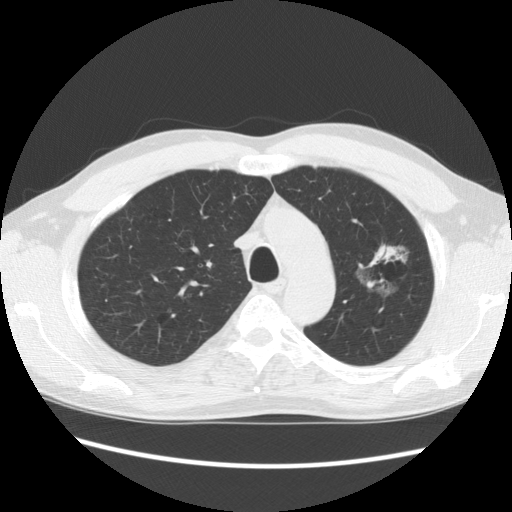
Low-dose screening chest CT, axial slice; second annual screen; lung window (W 1500 / L -600 HU); 2.5 mm slice thickness; 140 kVp; slice 104 of 139 in the series; 512 × 512 image matrix. Male, age 61 years at enrolment. Former smoker at enrolment.
Lesion marked by an expert reader, bounding box [x1, y1, x2, y2] px = [345, 224, 425, 301]. Reader record for this screening exam (exam-level; its link to the box is not recorded): non-calcified nodule or mass ≥4 mm, left upper lobe, 34 × 32 mm, poorly defined margins, mixed attenuation, pre-existing on the prior screen: yes; interval growth: no. Lung cancer was diagnosed 704 days after this screen (after the third annual screen): bronchiolo-alveolar adenocarcinoma, NOS, left upper lobe, well differentiated (G1), stage IB (AJCC 6th edition), 44 mm at pathology.